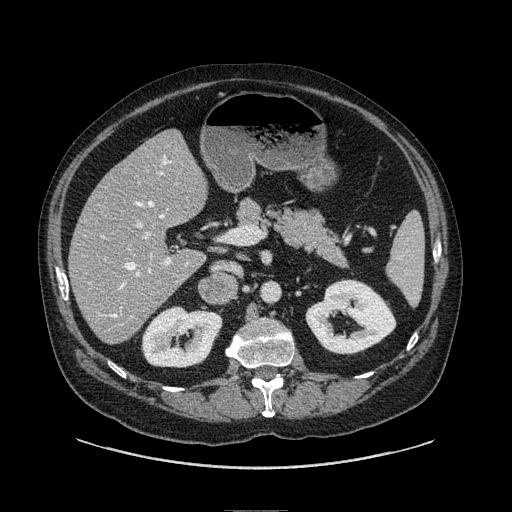
Contrast-enhanced abdominal CT, one axial slice; position 37 of 149 along the scan axis; soft-tissue window (W 400 / L 40 HU); 1.25 mm slice thickness; 512 × 512 image matrix, field of view 440 × 440 mm. Male patient. From the clinical record (not read from this slice): diagnosis: adrenocortical carcinoma; tumour side: right adrenal; tumour size at pathology: 7.5 cm; Ki-67 index: 15 %; stage (as recorded): 2.
Annotated regions visible in this slice (semi-automatically segmented with operator editing):
- mass: box from (x=200, y=275) to (x=236, y=301) px